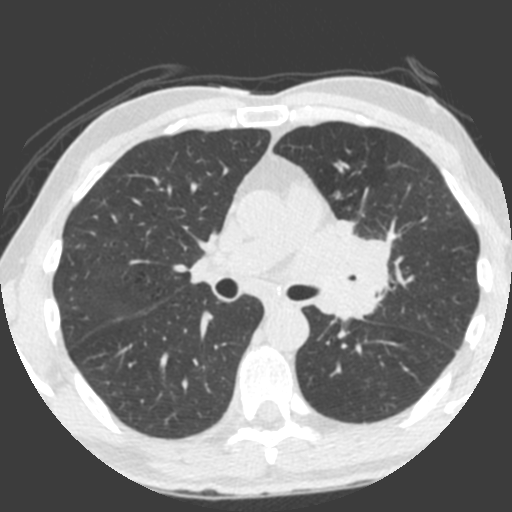
Axial slice from a low-dose chest CT screening exam, third screening round (two years after baseline), lung window (W 1500 / L -600 HU), 2 mm slice thickness. Male, age 55 years at enrolment. Current smoker at enrolment.
Lesion marked by an expert reader, bounding box [x1, y1, x2, y2] px = [309, 215, 399, 325]. Reader record for this screening exam (exam-level; its link to the box is not recorded): non-calcified nodule or mass ≥4 mm, left upper lobe, 49 × 29 mm, spiculated (stellate) margins, soft tissue attenuation, pre-existing on the prior screen: yes; interval growth: yes. Official screen result: positive, other.